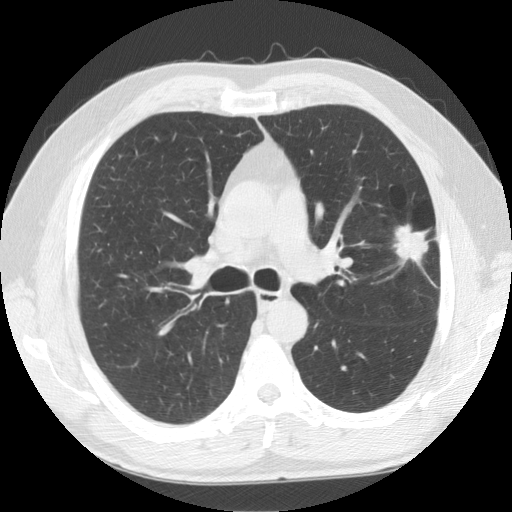
Low-dose screening chest CT, one axial slice. Reconstruction kernel STANDARD. 120 kVp. Lung window (W 1500 / L -600 HU). 2.5 mm slice thickness. 512 × 512 image matrix, field of view 360 × 360 mm.
Structures marked on this image (manually delineated by an expert):
- lesion 1 (tumor, upper lobe of left lung): box from (x=393, y=224) to (x=429, y=261) px